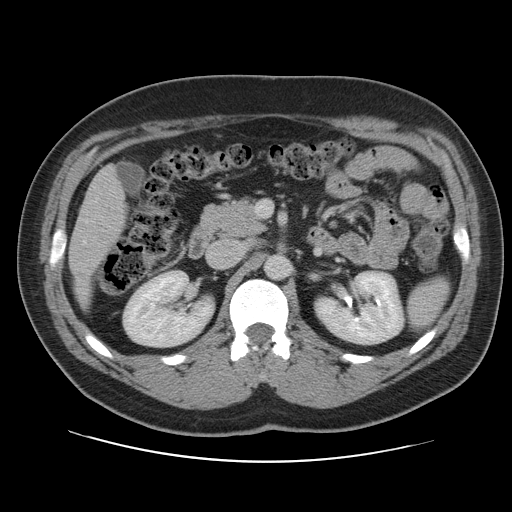
Contrast-enhanced abdominal CT, one axial slice; position 54 of 109 along the scan axis; 120 kVp; intravenous contrast given; soft-tissue window (W 400 / L 40 HU); 5 mm slice thickness; 512 × 512 image matrix, field of view 402 × 402 mm. Male patient, age 35 years. From the clinical record (not read from this slice): diagnosis: colorectal cancer liver metastases, imaged before liver resection.
Structures marked on this image (expert manual segmentation):
- liver: bounding box <70,169,126,306> (left, top, right, bottom; pixels)
- planned liver remnant (the part of the liver to remain after resection): <70,168,126,307>